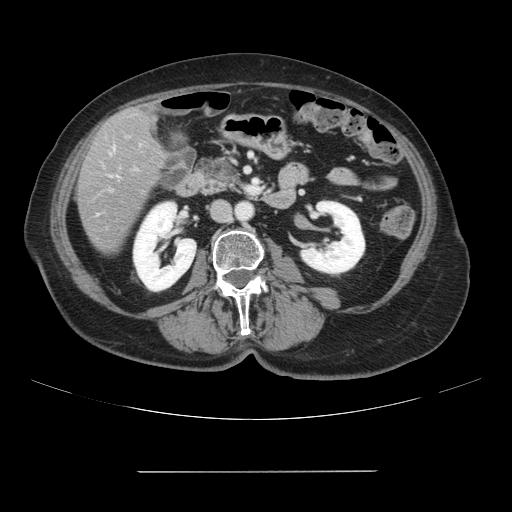
Contrast-enhanced abdominal CT, one axial slice. Slice 23 of 111 in the series (ordered by position). Intravenous contrast given. Soft-tissue window (W 400 / L 40 HU). 512 × 512 image matrix. Female patient, age 74 years. From the clinical record (not read from this slice): diagnosis: colorectal cancer liver metastases, imaged before liver resection; multiple liver metastases: yes.
Outlined on this slice (expert manual segmentation):
- liver: box from (x=77, y=106) to (x=167, y=255) px